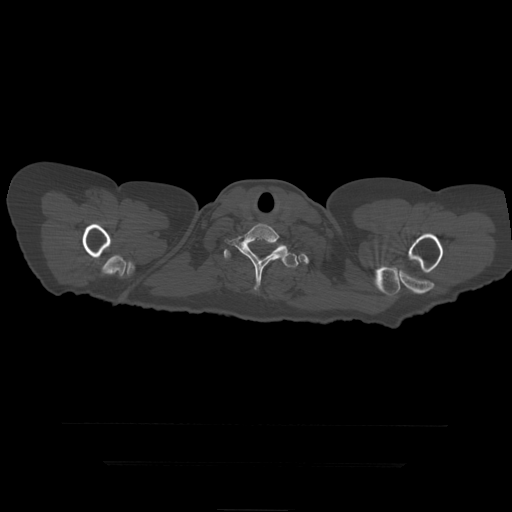
CT including the spine, one axial slice. Position 385 of 399 along the scan axis. 120 kVp. Bone window (W 1800 / L 400 HU). 512 × 512 image matrix, field of view 450 × 450 mm. Patient age 41 years. From the clinical record (not read from this slice): primary cancer: breast.
Structures marked on this image (semi-automatic segmentation, software-assisted and operator-edited):
- T1 vertebra: bounding box [x1, y1, x2, y2] px = [225, 223, 298, 291]
- T2 vertebra: [224, 248, 299, 268]